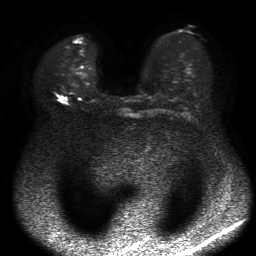
Breast MRI, one axial slice. Slice 32 of 50 in the series (ordered by position). Diffusion-weighted series; image 2 of 4 stored at this slice position (different b-values; order by instance number). 1.5 T. 4 mm slice thickness. 256 × 256 image matrix. Female patient.
Structures marked on this image (manually delineated by an expert):
- tumour on diffusion-weighted imaging: bounding box (x1, y1, x2, y2) in pixels: (61, 96, 67, 103)